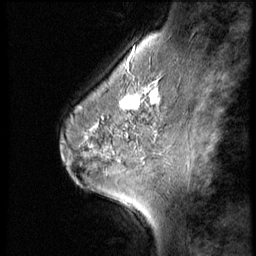
Breast MRI (dynamic contrast-enhanced), one sagittal slice; position 40 of 56 along the scan axis; 3 images stored at this slice position (order not interpretable as contrast timing); 1.5 T; TE 4.2 ms, TR 9 ms; 2.5 mm slice thickness; 256 × 256 image matrix. Patient: female, 45 years. Case-level facts recorded for this patient, not image findings: setting: breast cancer imaged before/during neoadjuvant chemotherapy; receptor status: HR-positive, HER2-negative.
Structures marked on this image (semi-automatically segmented with operator editing):
- analysis volume of interest (the breast-tissue region the enhancement analysis was run in; not a lesion): bounding box [x1, y1, x2, y2] px = [102, 77, 166, 129]
- tumour enhancement mask (voxels above the 140 % enhancement threshold inside the analysis volume of interest): [102, 77, 160, 129]